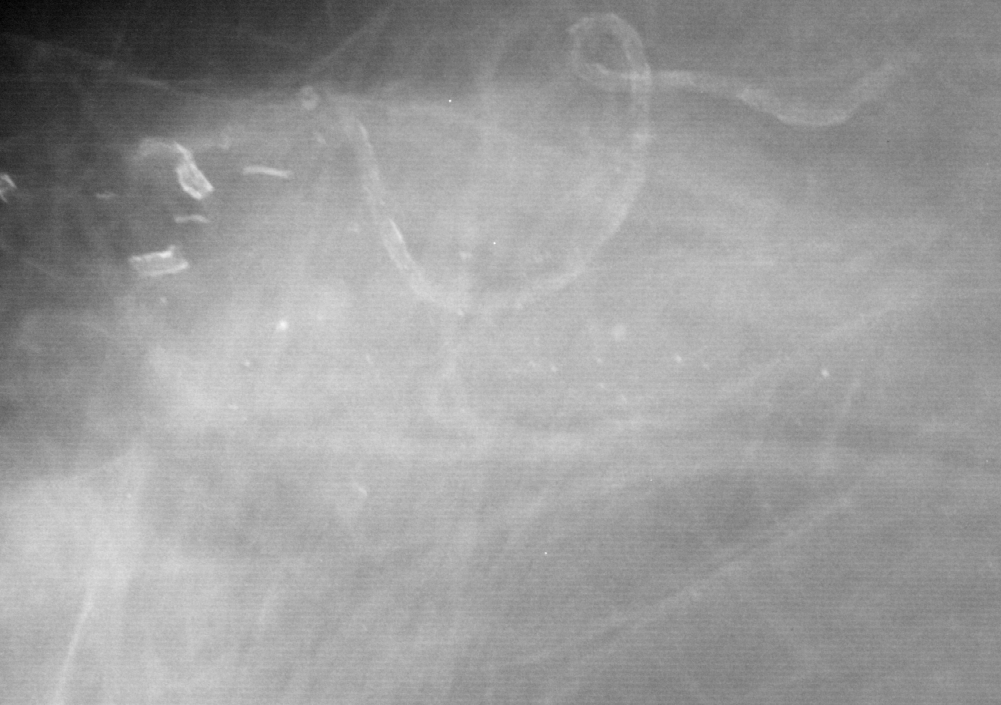
Region of interest cut from a scanned film mammogram (one marked finding); right breast; CC view; BI-RADS breast density category 2 (scale 1–4).
Calcifications, morphology punctate, distribution segmental; BI-RADS assessment category 4; pathology result (as recorded, not read from the image): benign.